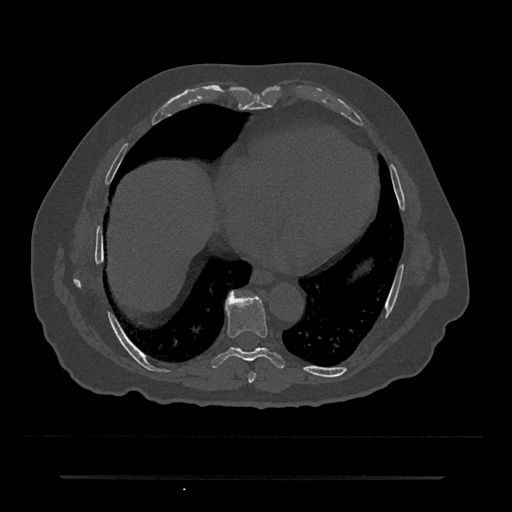
CT including the spine, one axial slice. Slice 329 of 797 in the series (ordered by position). Reconstruction kernel Br40s/3. 120 kVp. Bone window (W 1800 / L 400 HU). 0.5 mm slice thickness. 512 × 512 image matrix, field of view 437 × 437 mm. Male patient, age 69 years. Case-level facts recorded for this patient, not image findings: primary cancer: prostate.
Annotated regions visible in this slice (semi-automatic segmentation, software-assisted and operator-edited):
- T7 vertebra: bounding box [x1, y1, x2, y2] px = [248, 372, 256, 383]
- T8 vertebra: [211, 292, 285, 369]